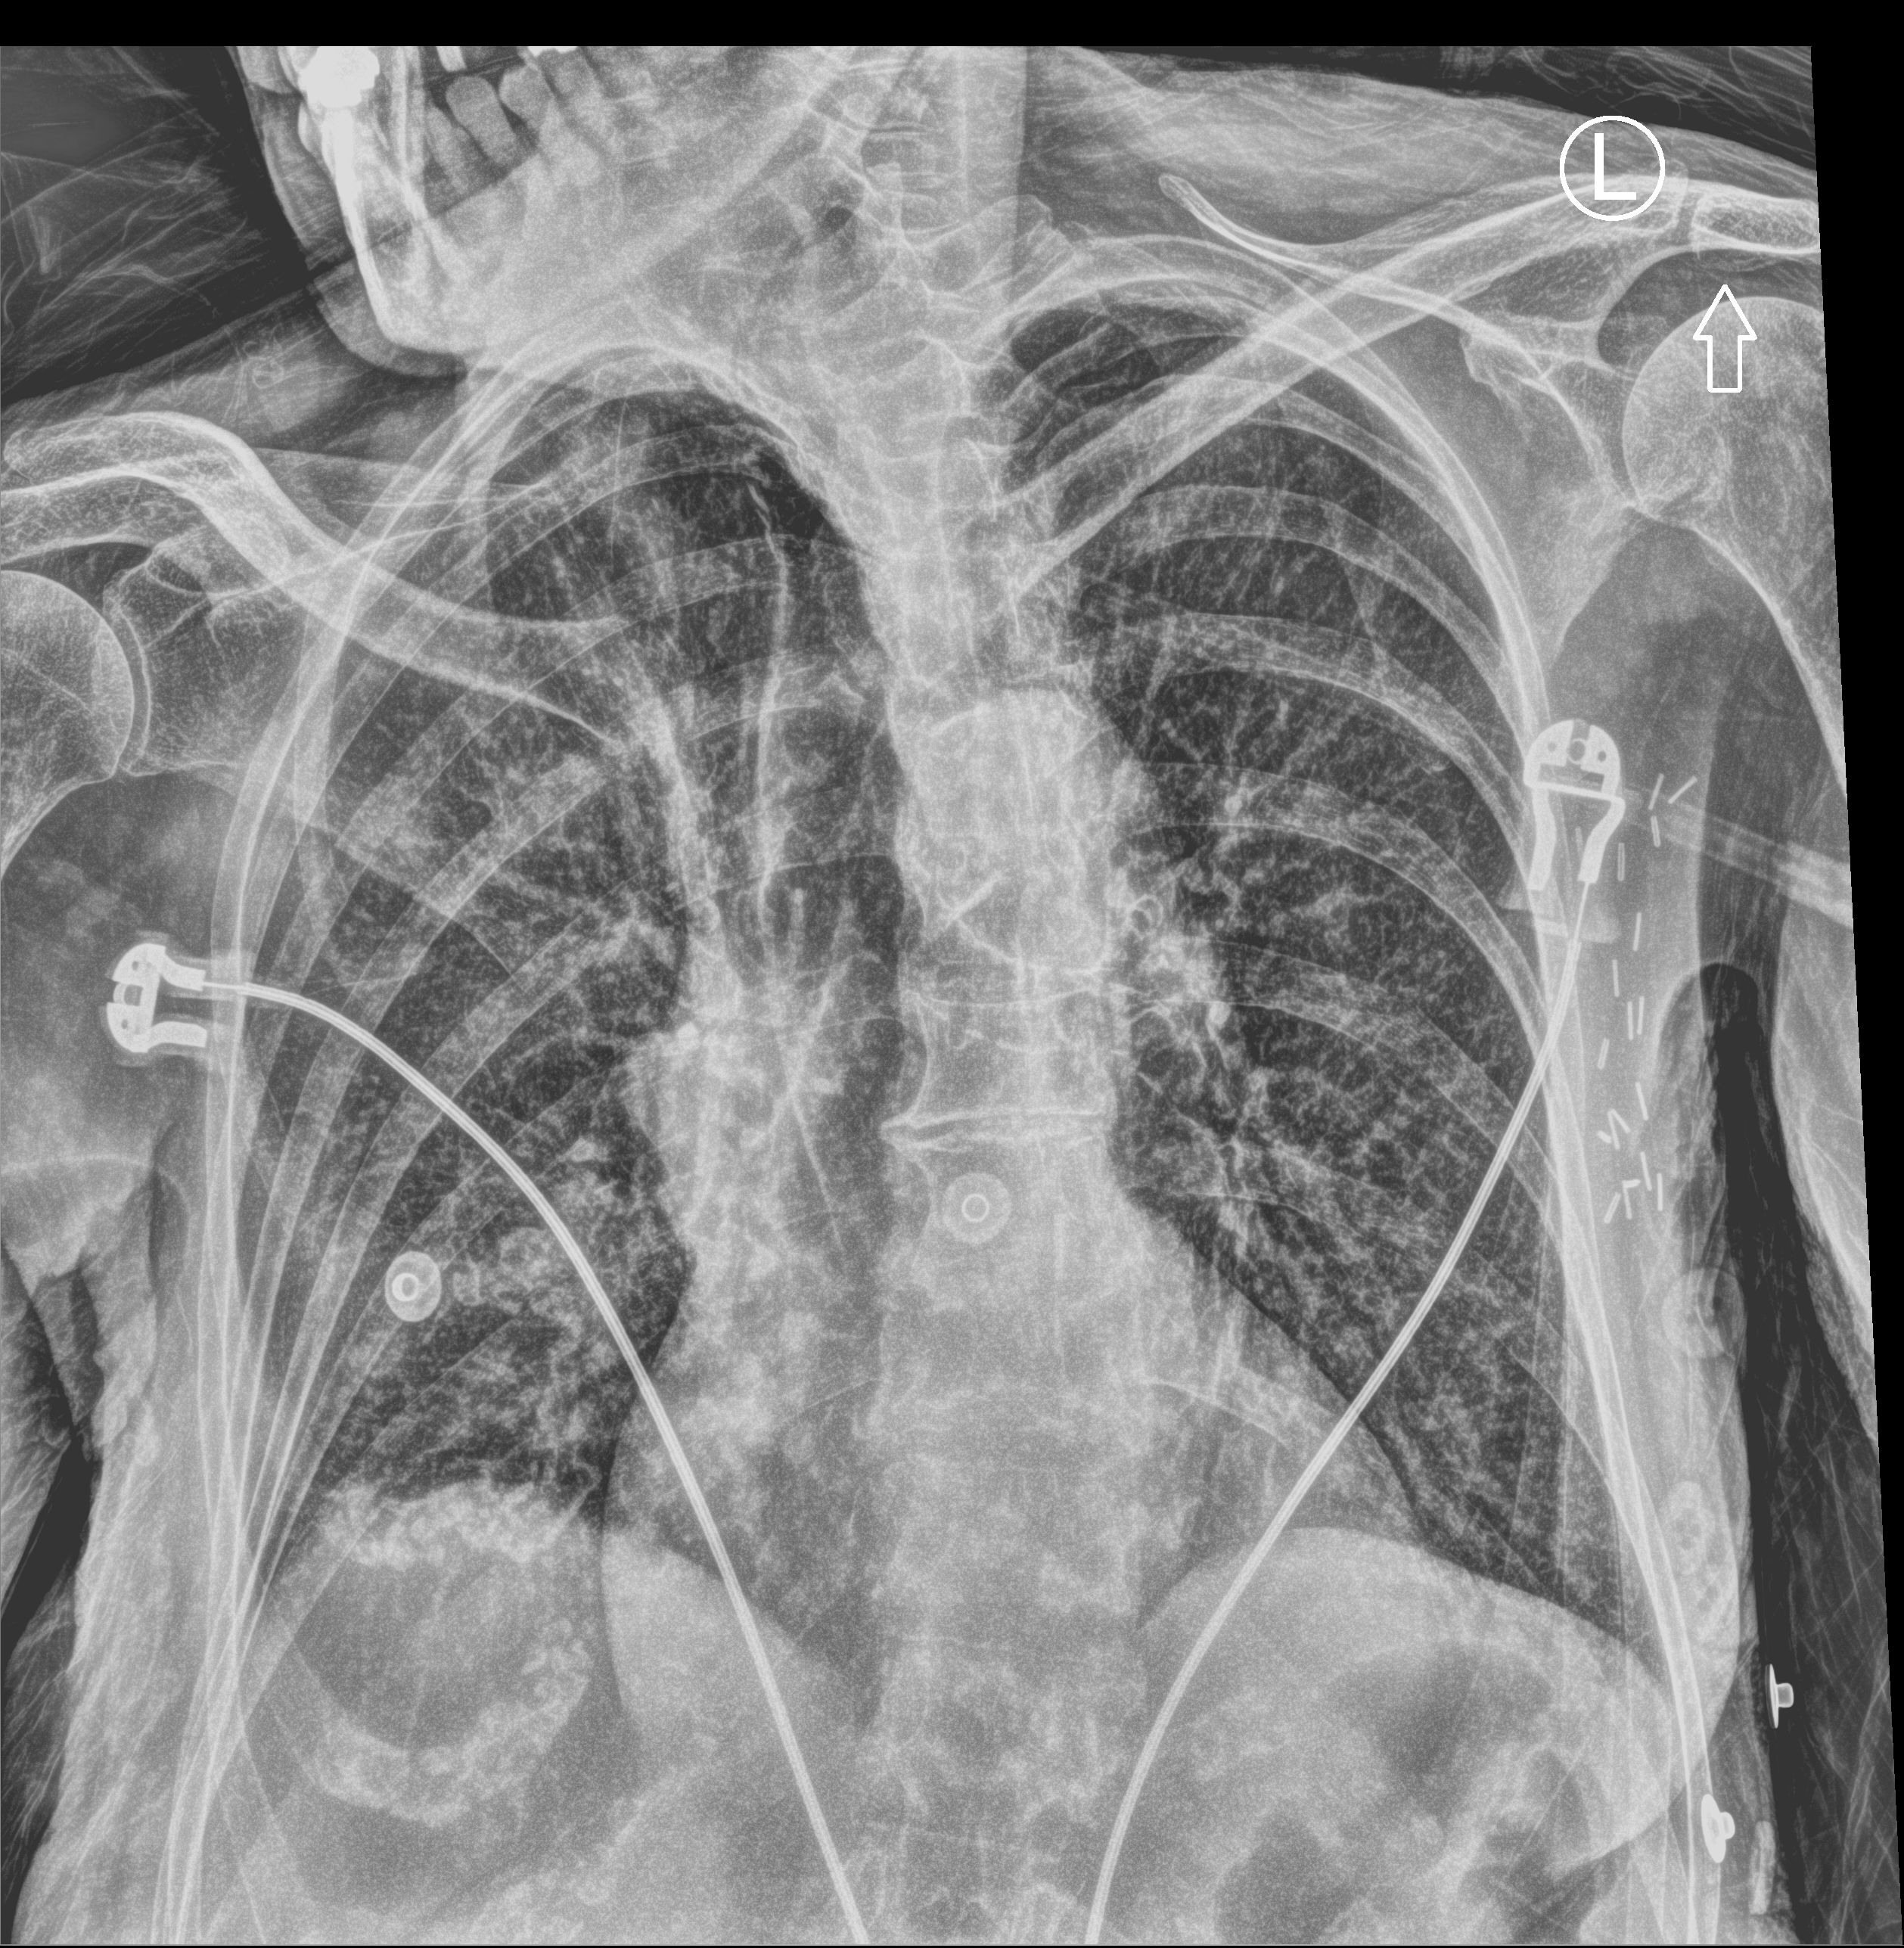
Bedside chest radiograph (computed radiography), anteroposterior (AP) projection. Patient hospitalised with COVID-19; female, aged 75–90 years.
From the hospital-stay record, not from the radiograph (when in the stay this image was taken is not recorded):
- mechanically ventilated during this hospital stay: no
- admitted to intensive care during this hospital stay: no